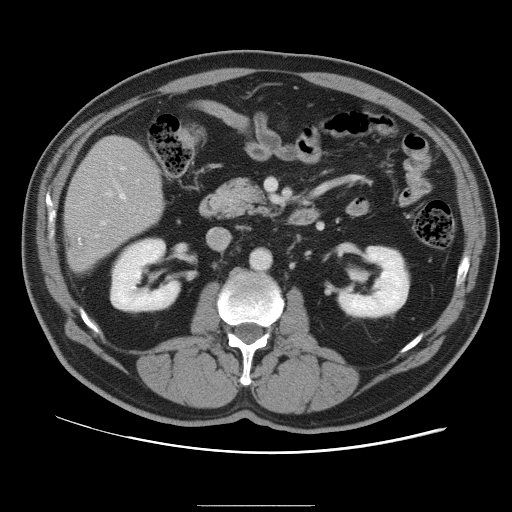
Contrast-enhanced abdominal CT, one axial slice. Slice 39 of 105 in the series (ordered by position). Intravenous contrast given. Soft-tissue window (W 400 / L 40 HU). 512 × 512 image matrix. Male patient, age 64 years. Case-level facts recorded for this patient, not image findings: diagnosis: colorectal cancer liver metastases, imaged before liver resection; multiple liver metastases: yes; largest metastasis: 3 cm; disease in both lobes: yes.
Structures marked on this image (manually delineated by an expert):
- hepatic veins: box from (x=101, y=194) to (x=126, y=225) px
- liver: (x=66, y=136)–(x=164, y=272)
- planned liver remnant (the part of the liver to remain after resection): (x=66, y=136)–(x=163, y=245)
- portal vein (with intrahepatic branches): (x=96, y=167)–(x=125, y=237)
- liver metastasis: (x=69, y=237)–(x=86, y=259)